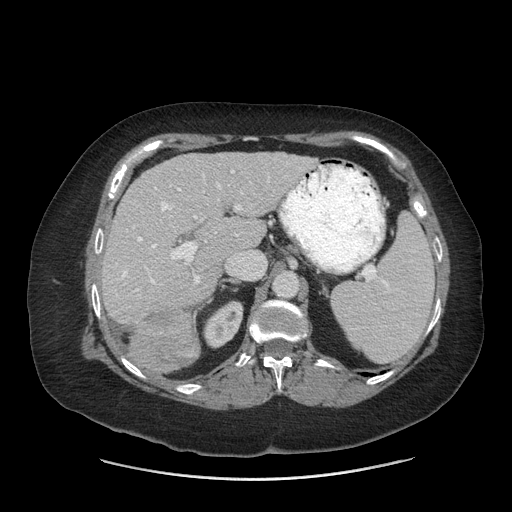
Contrast-enhanced abdominal CT (liver protocol), one axial slice. Position 42 of 69 along the scan axis. Soft-tissue window (W 400 / L 40 HU). 2.5 mm slice thickness. 512 × 512 image matrix. From the clinical record (not read from this slice): diagnosis: hepatocellular carcinoma (patient treated with transarterial chemoembolisation; whether this scan precedes or follows treatment is not stated here); TNM stage (as recorded): Stage-IIIB; Child-Pugh class: A; tumour nodularity: multinodular.
Structures marked on this image (semi-automatically segmented with operator editing):
- liver parenchyma outside the tumour (the mass and vessels are separate outlines, so this box may not span the whole liver): bounding box (x1, y1, x2, y2) in pixels: (102, 152, 316, 326)
- mass: (127, 304, 201, 374)
- liver vessels: (121, 163, 288, 292)